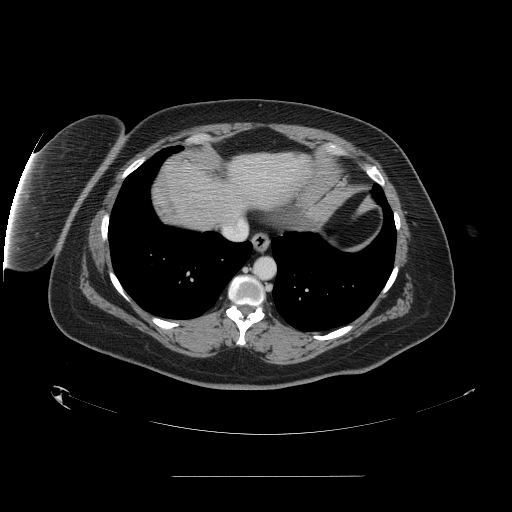
Contrast-enhanced abdominal CT, one axial slice; position 140 of 164 along the scan axis; 120 kVp; intravenous contrast given; soft-tissue window (W 400 / L 40 HU); 512 × 512 image matrix, field of view 495 × 495 mm. Female patient, age 52 years. From the clinical record (not read from this slice): diagnosis: colorectal cancer liver metastases, imaged before liver resection; multiple liver metastases: yes; largest metastasis: 3.5 cm; disease in both lobes: no.
Annotated regions visible in this slice (expert manual segmentation):
- hepatic veins: bounding box [x1, y1, x2, y2] px = [224, 219, 245, 238]
- liver: [163, 153, 310, 230]
- planned liver remnant (the part of the liver to remain after resection): [183, 153, 311, 224]